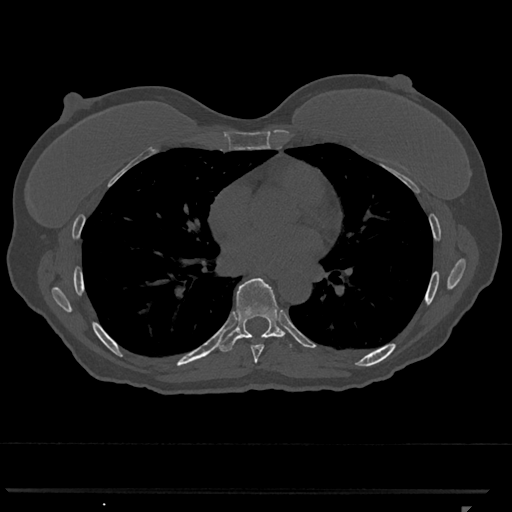
CT including the spine, one axial slice; position 683 of 793 along the scan axis; reconstruction kernel Br40s/3; 120 kVp; bone window (W 1800 / L 400 HU); 0.5 mm slice thickness; 512 × 512 image matrix, field of view 380 × 380 mm. Female patient, age 62 years. Case-level facts recorded for this patient, not image findings: primary cancer: renal.
Annotated regions visible in this slice (semi-automatic segmentation, software-assisted and operator-edited):
- T7 vertebra: box from (x=251, y=344) to (x=264, y=364) px
- T8 vertebra: (x=219, y=278)–(x=292, y=352)